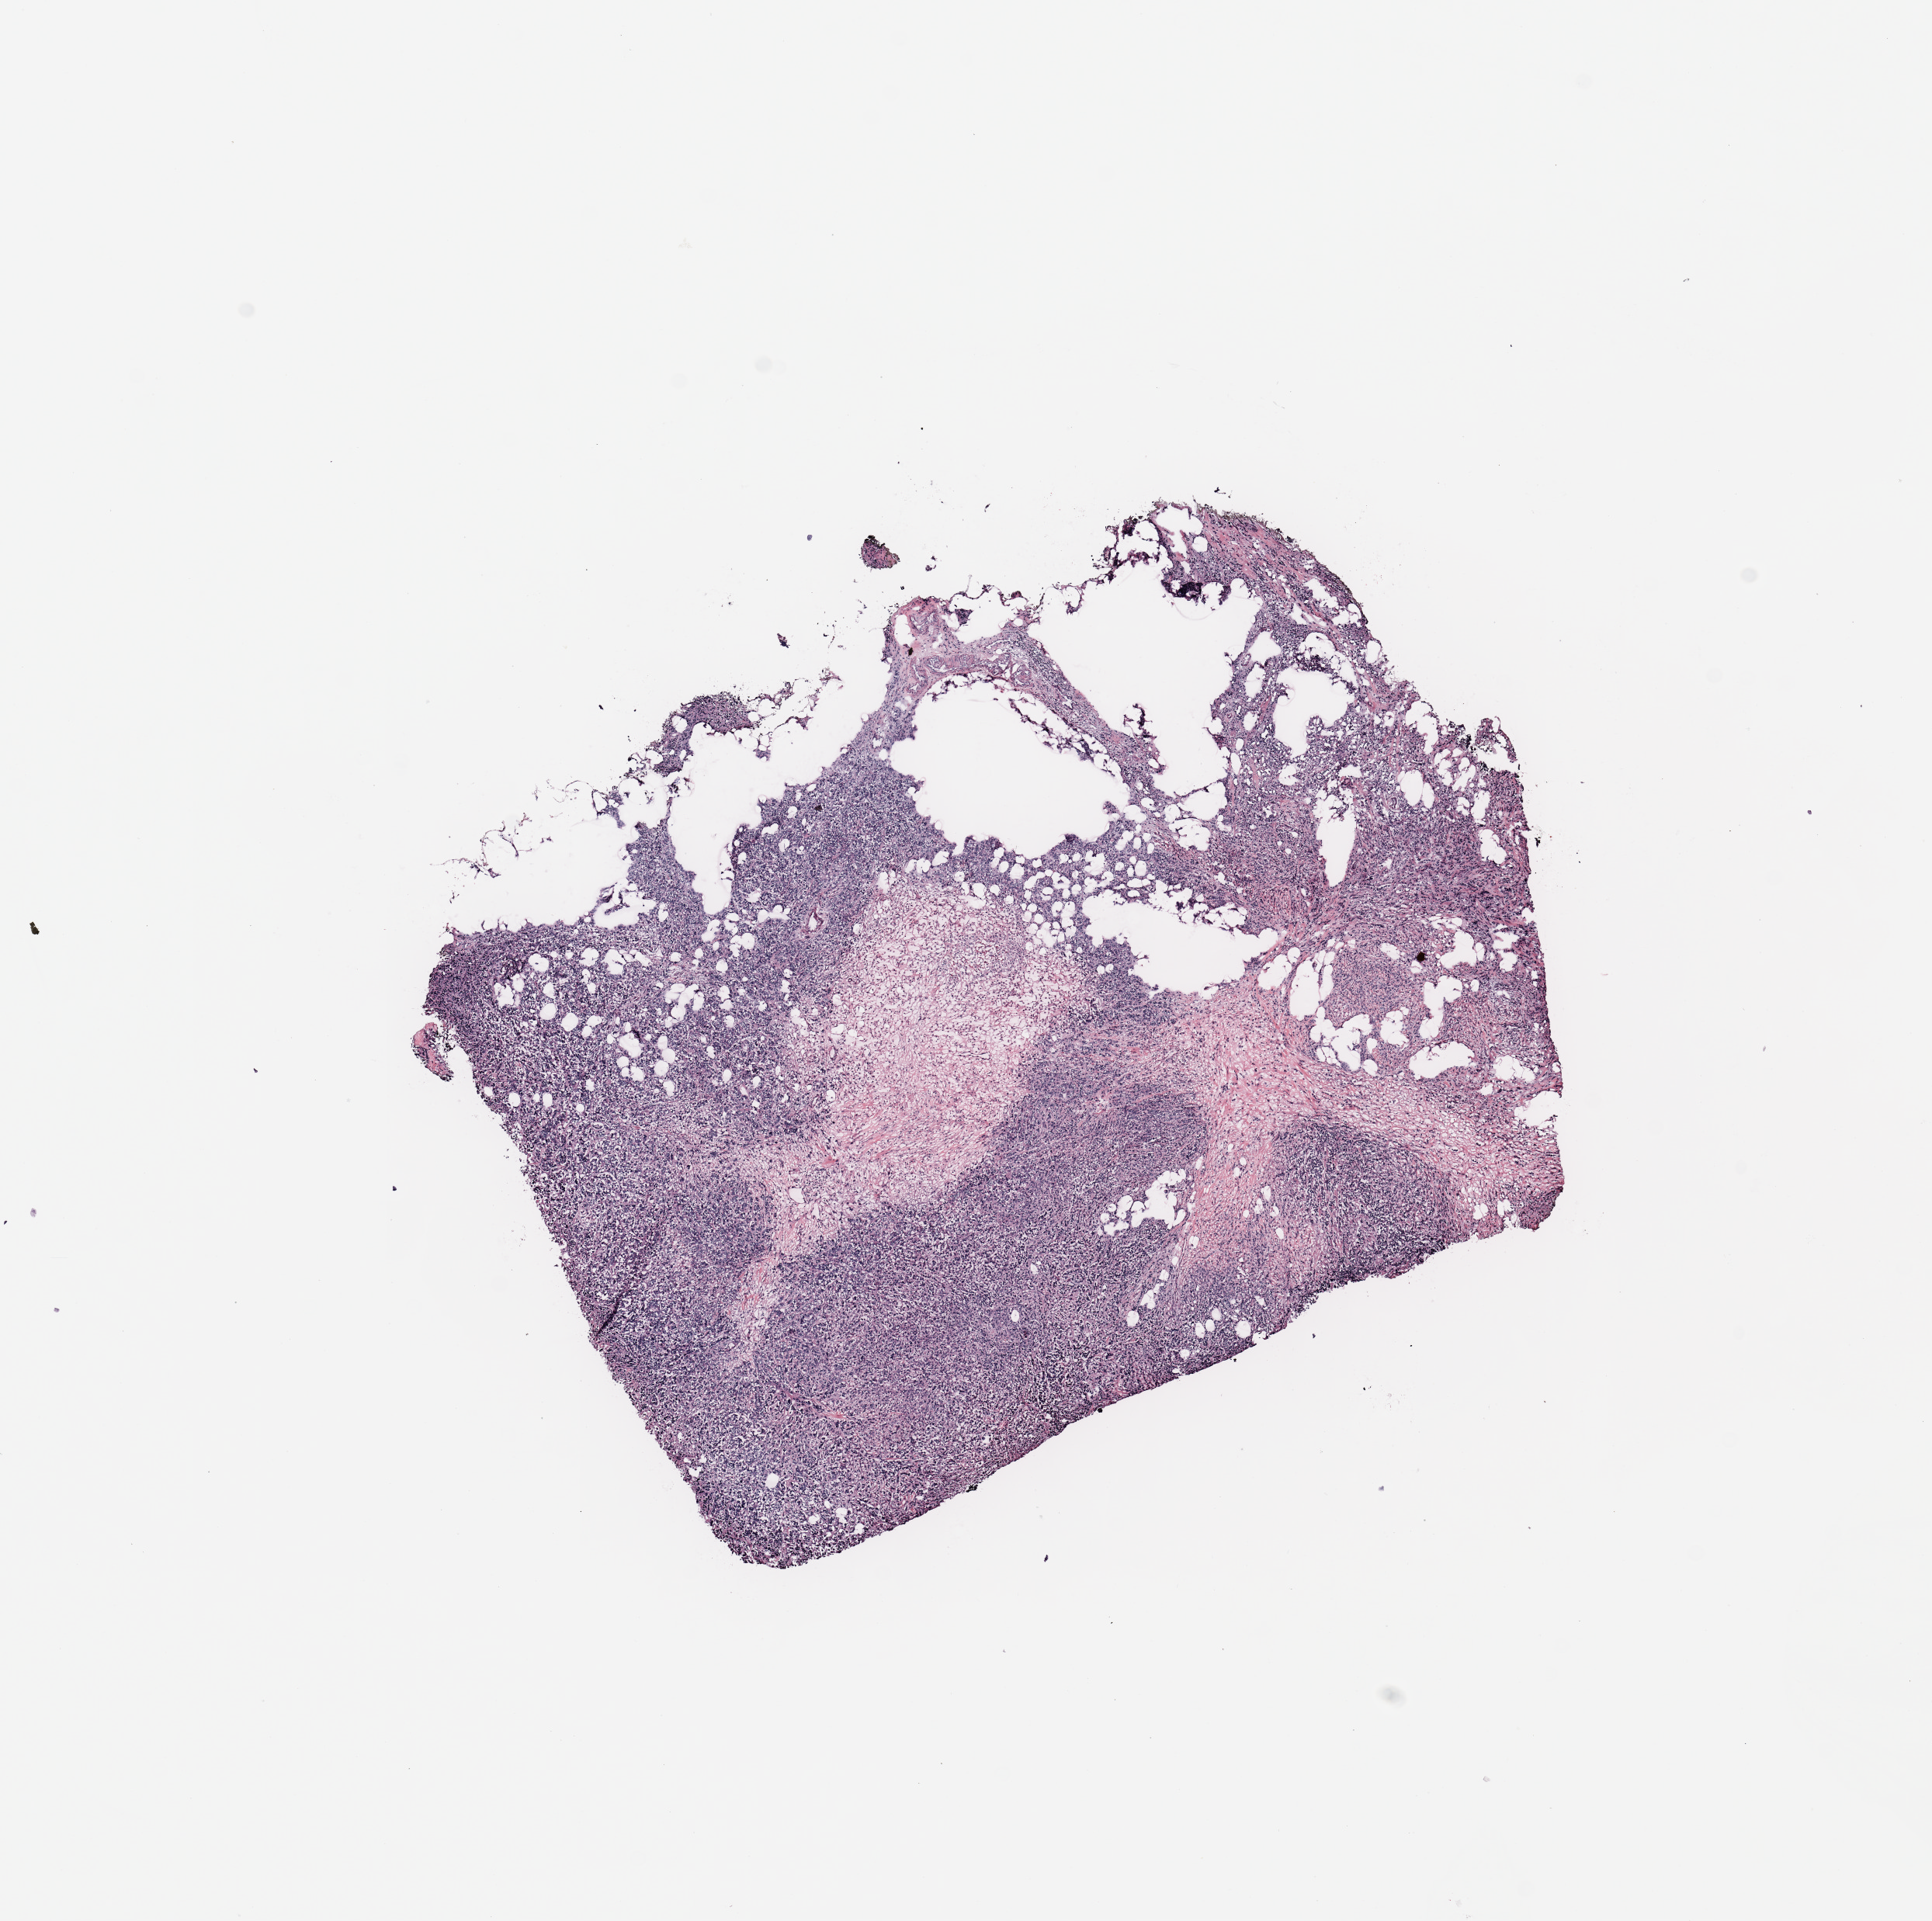
Hematoxylin and eosin (H&E) stained whole-slide image — low-resolution overview of the scanned area, about 9.8 x 9.8 mm. 61-year-old female patient.
Specimen: breast, tumour tissue.